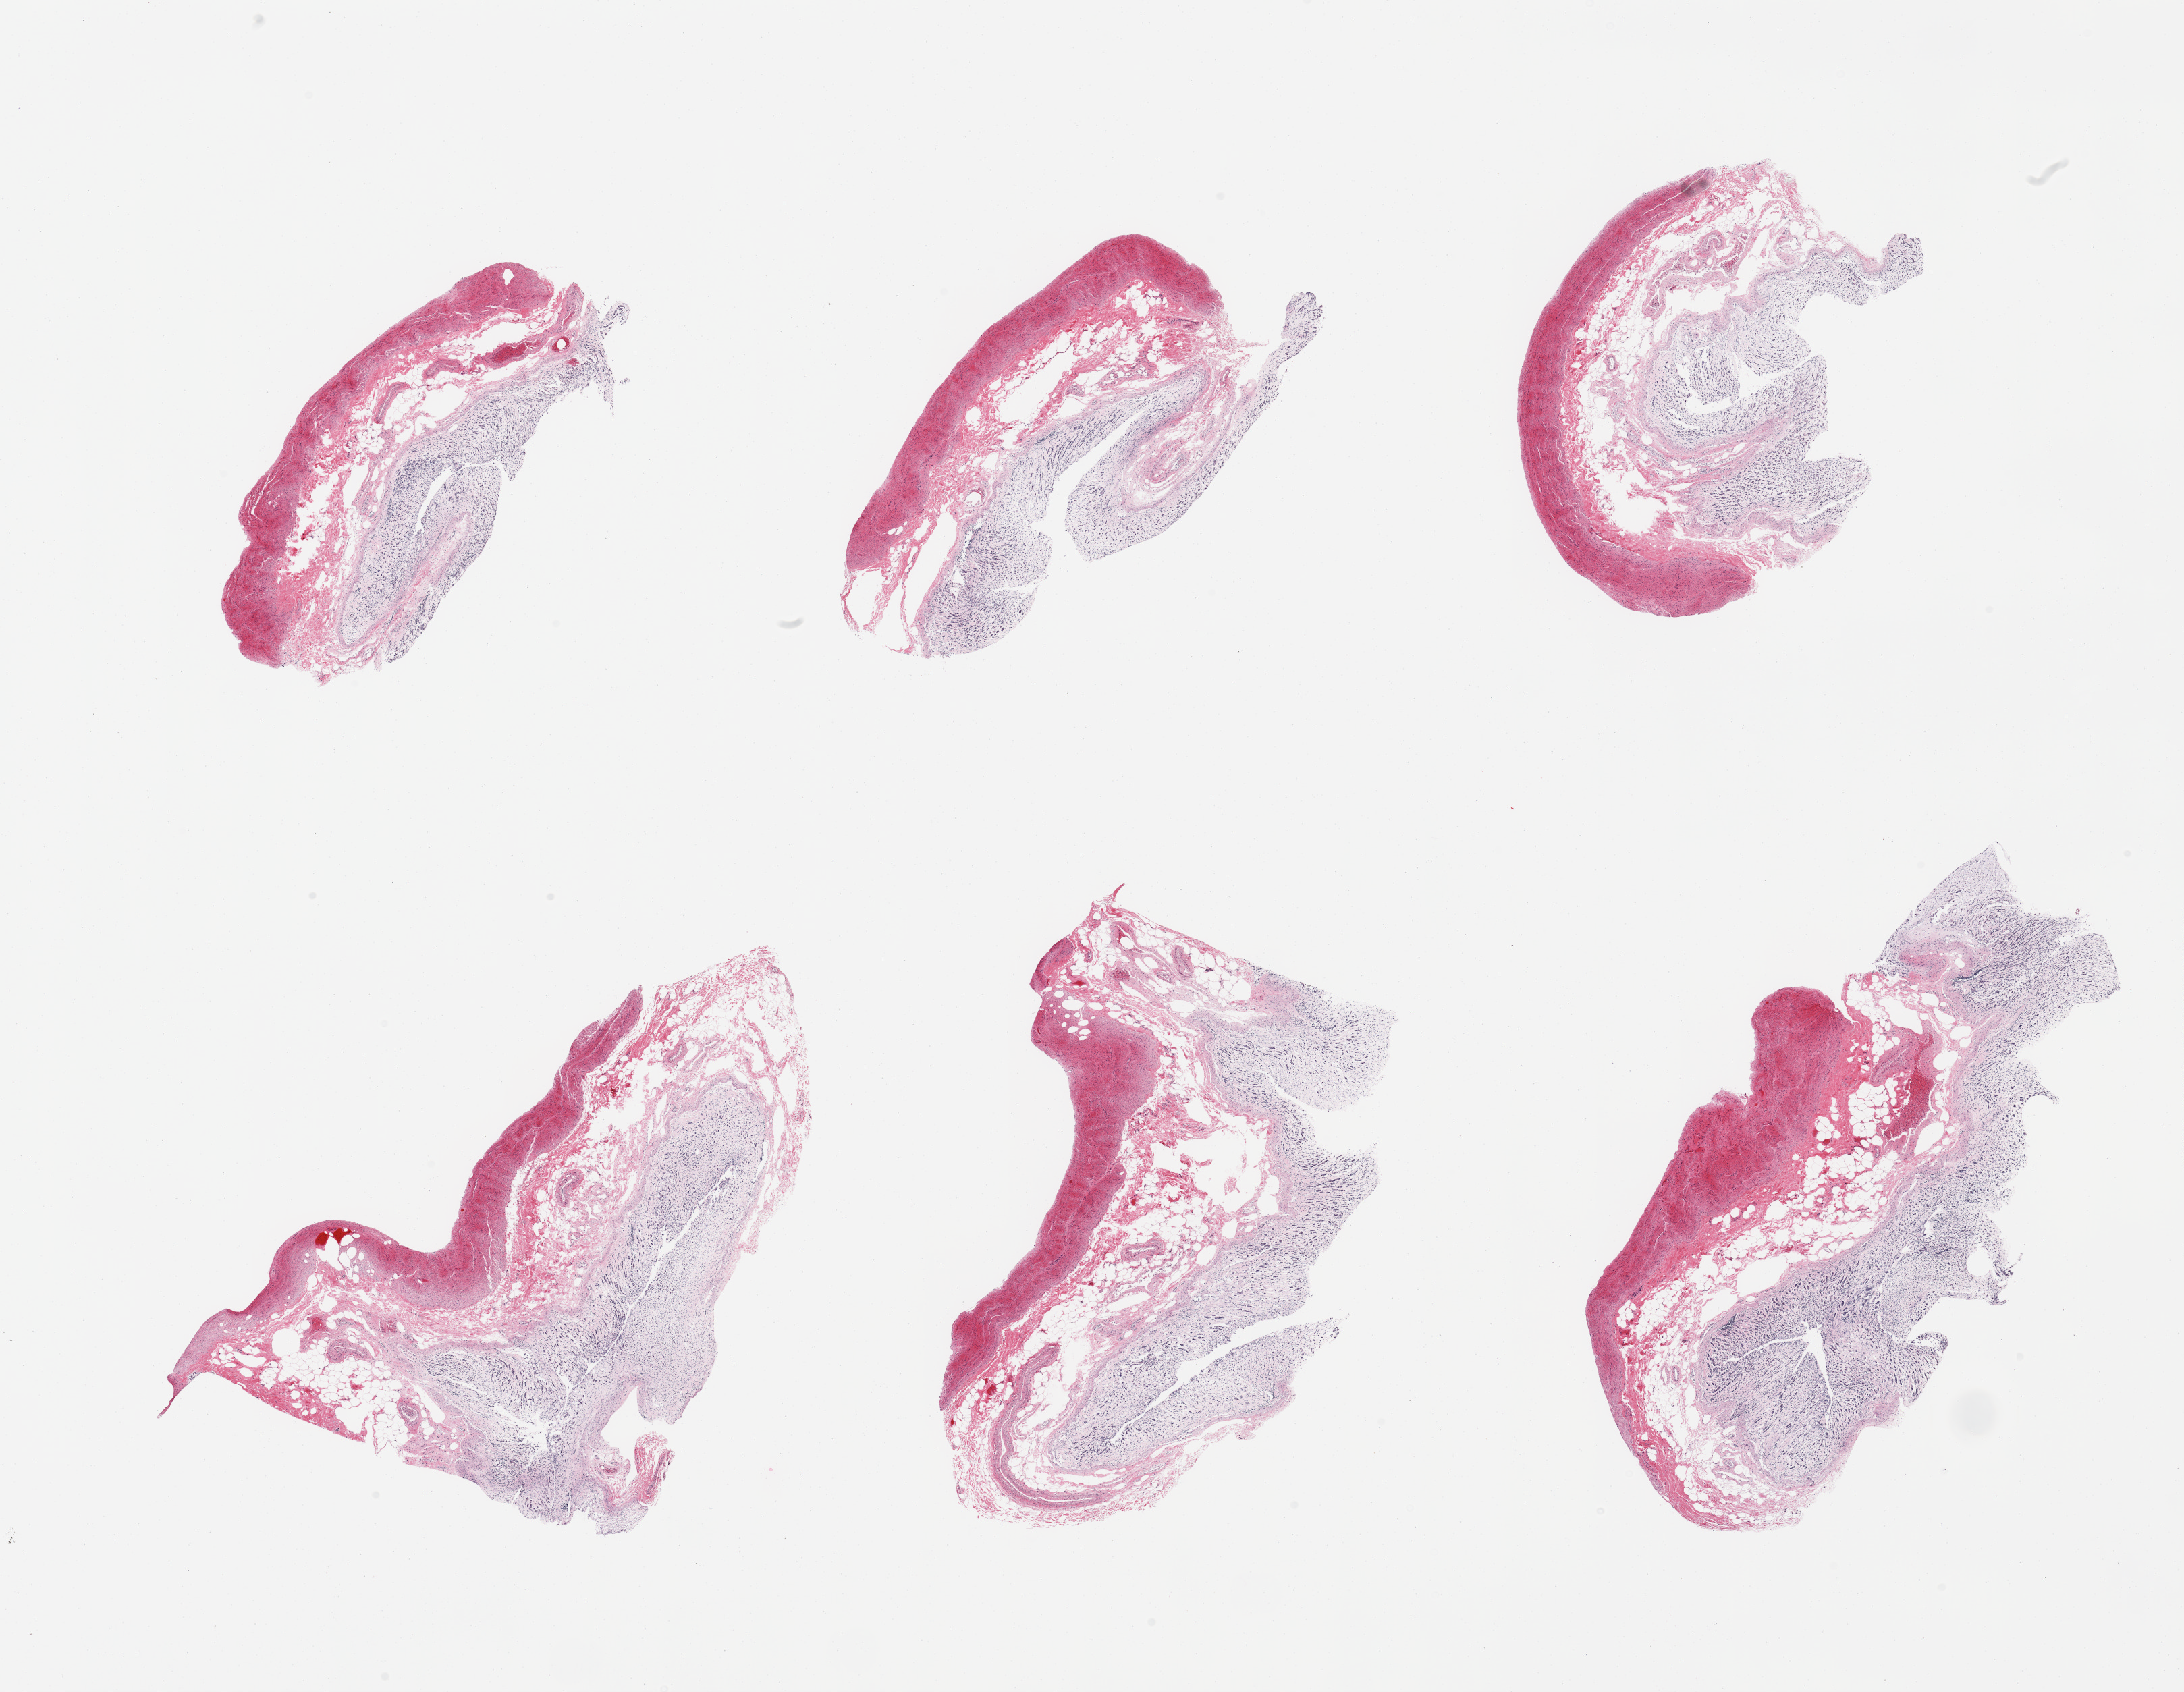
Digitized haematoxylin and eosin-stained section, brightfield, whole scanned area (about 25.6 x 19.8 mm, slide scanned at 20x) shown as a low-resolution overview. Male donor.
Specimen: PAXgene-fixed, paraffin-embedded tissue; target tissue: stomach; donor tissue sample.